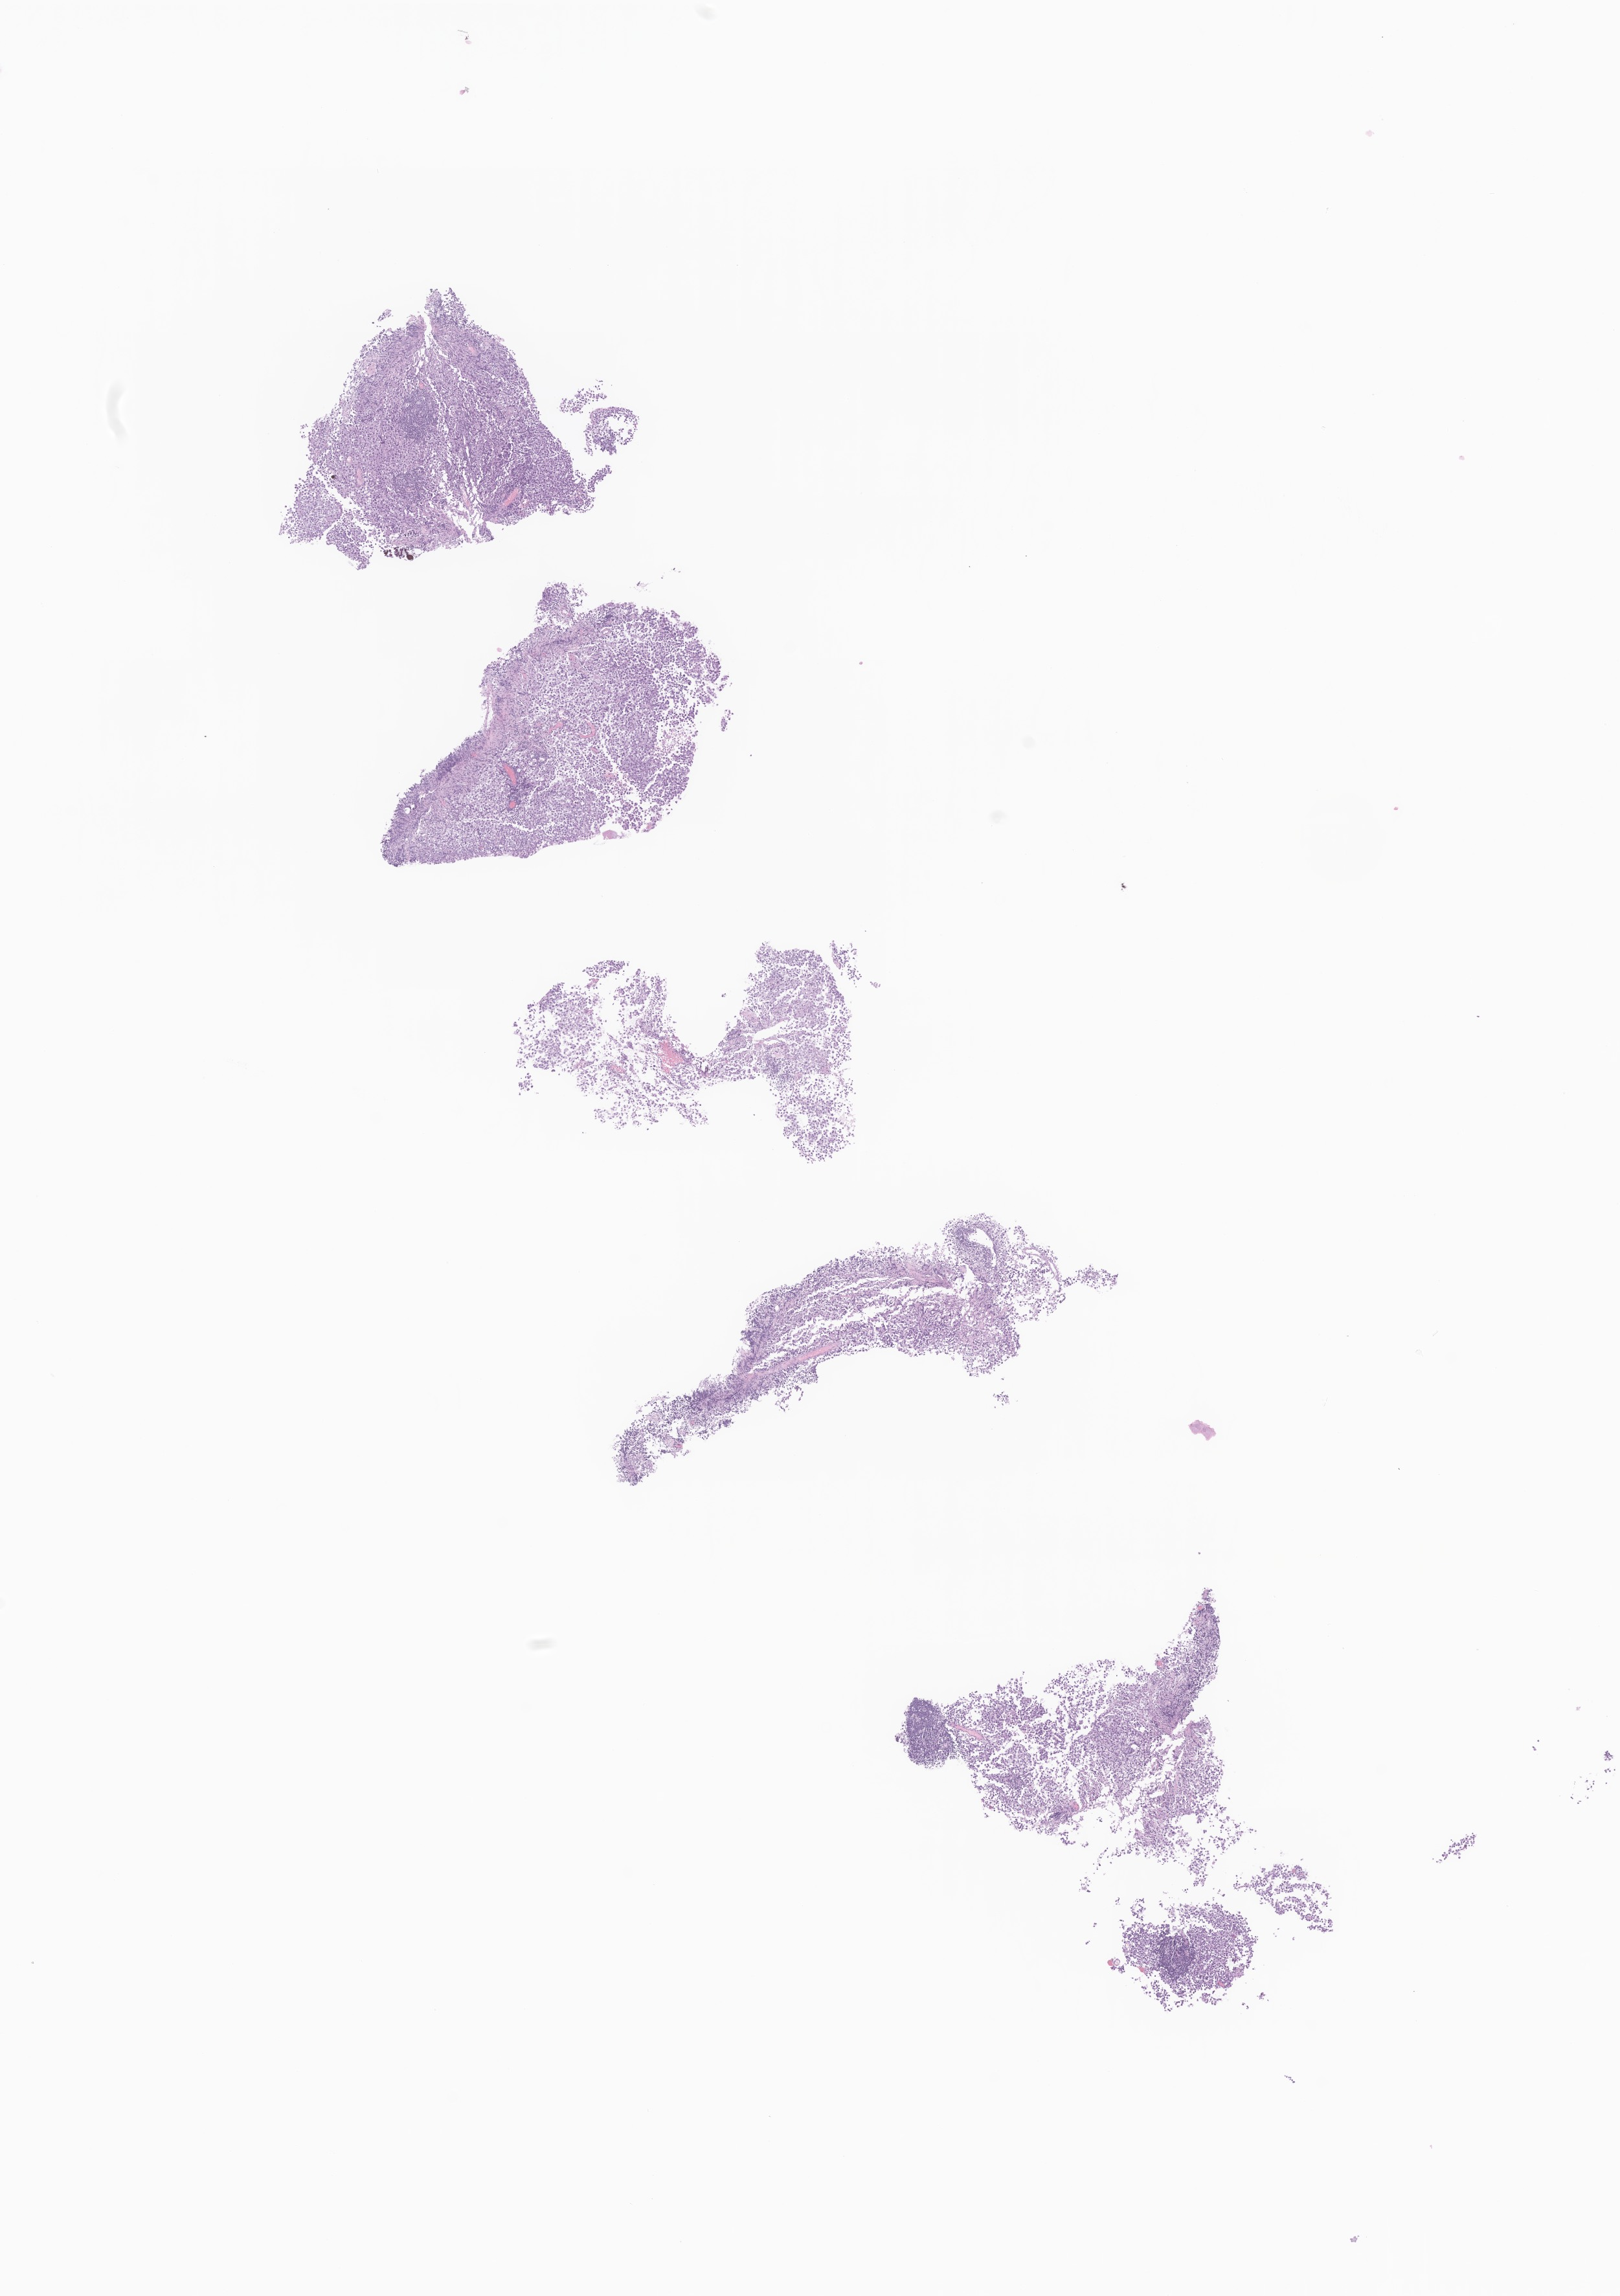
Whole-slide image, H&E stain of tumor tissue from the brain — a low-resolution overview of the entire scanned area, about 10.5 x 15.0 mm, FFPE section. Patient: male, age 217 months (18 years 1 month).
- diagnosis (ICD-O-3 morphology term): Germinoma